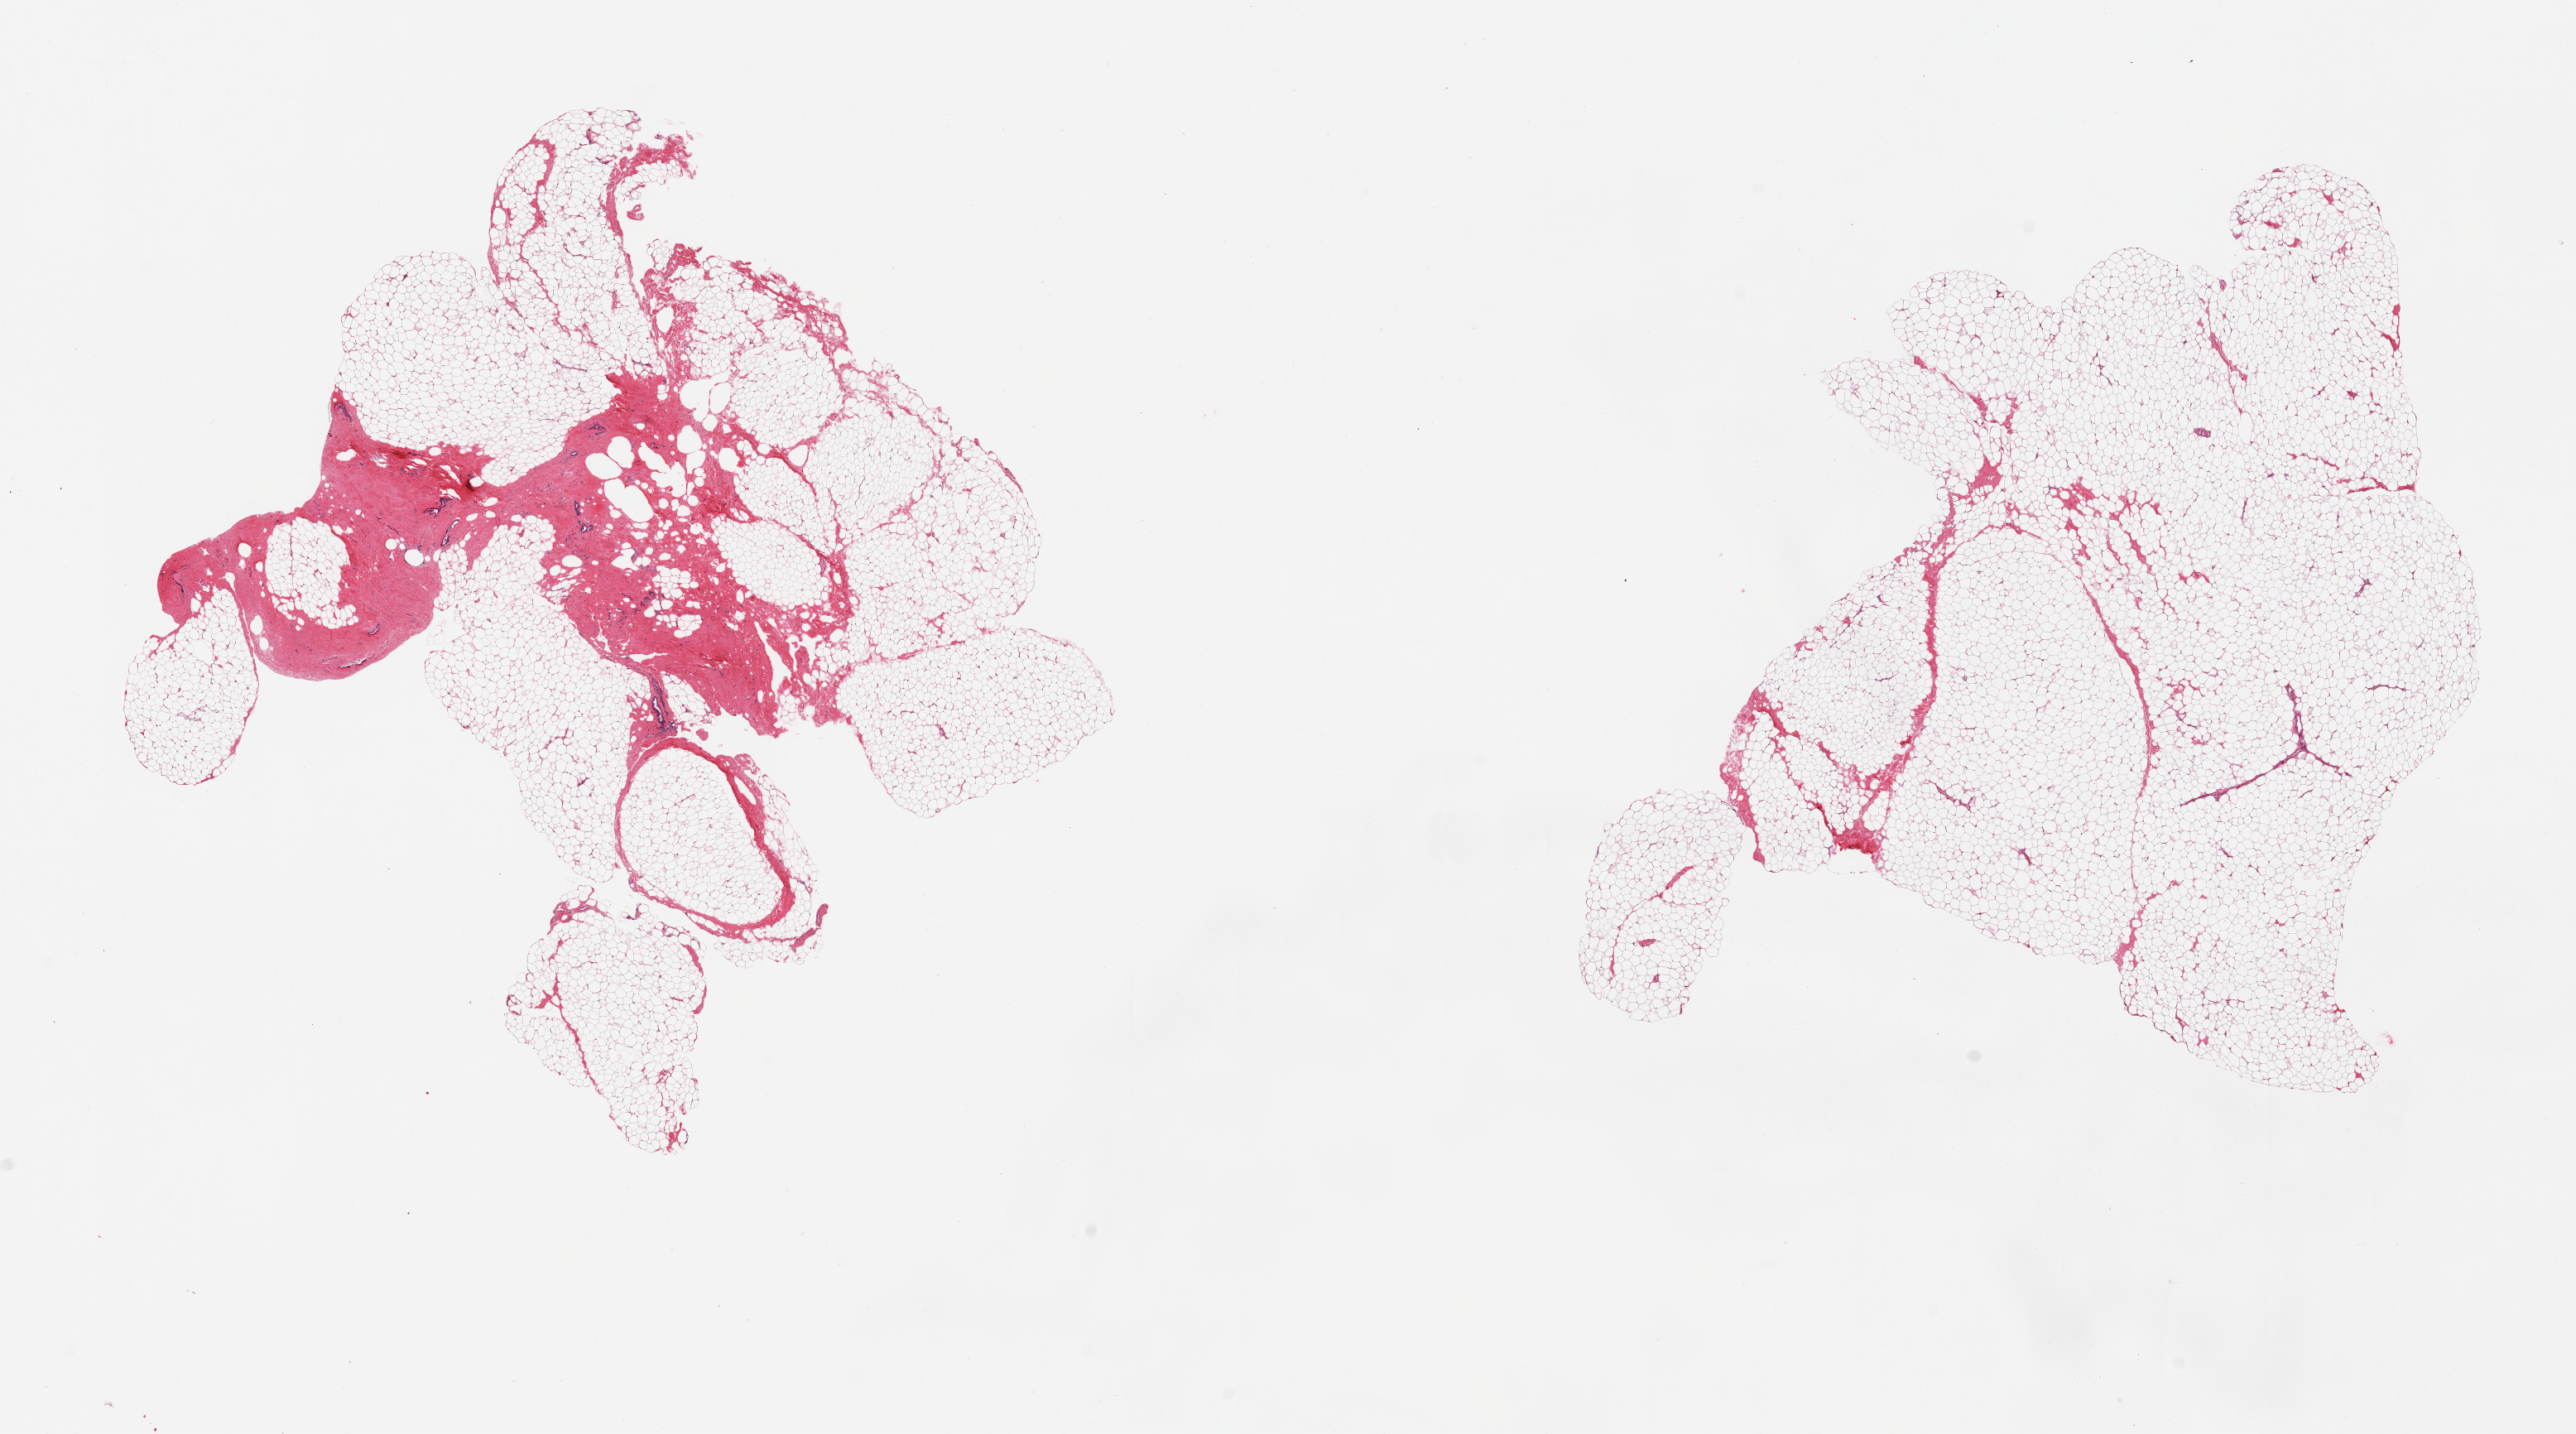
Digitized hematoxylin and eosin (H&E)-stained section — shown as a low-resolution overview of the whole scanned area (about 24.6 x 13.7 mm). PAXgene-fixed, paraffin-embedded tissue. Target tissue: breast. Donor tissue sample. Male donor.
Reviewer comment on this tissue sample: 2 pieces focal gynecomastoid stromal hyperplasia; few ductal elements seen in one section.